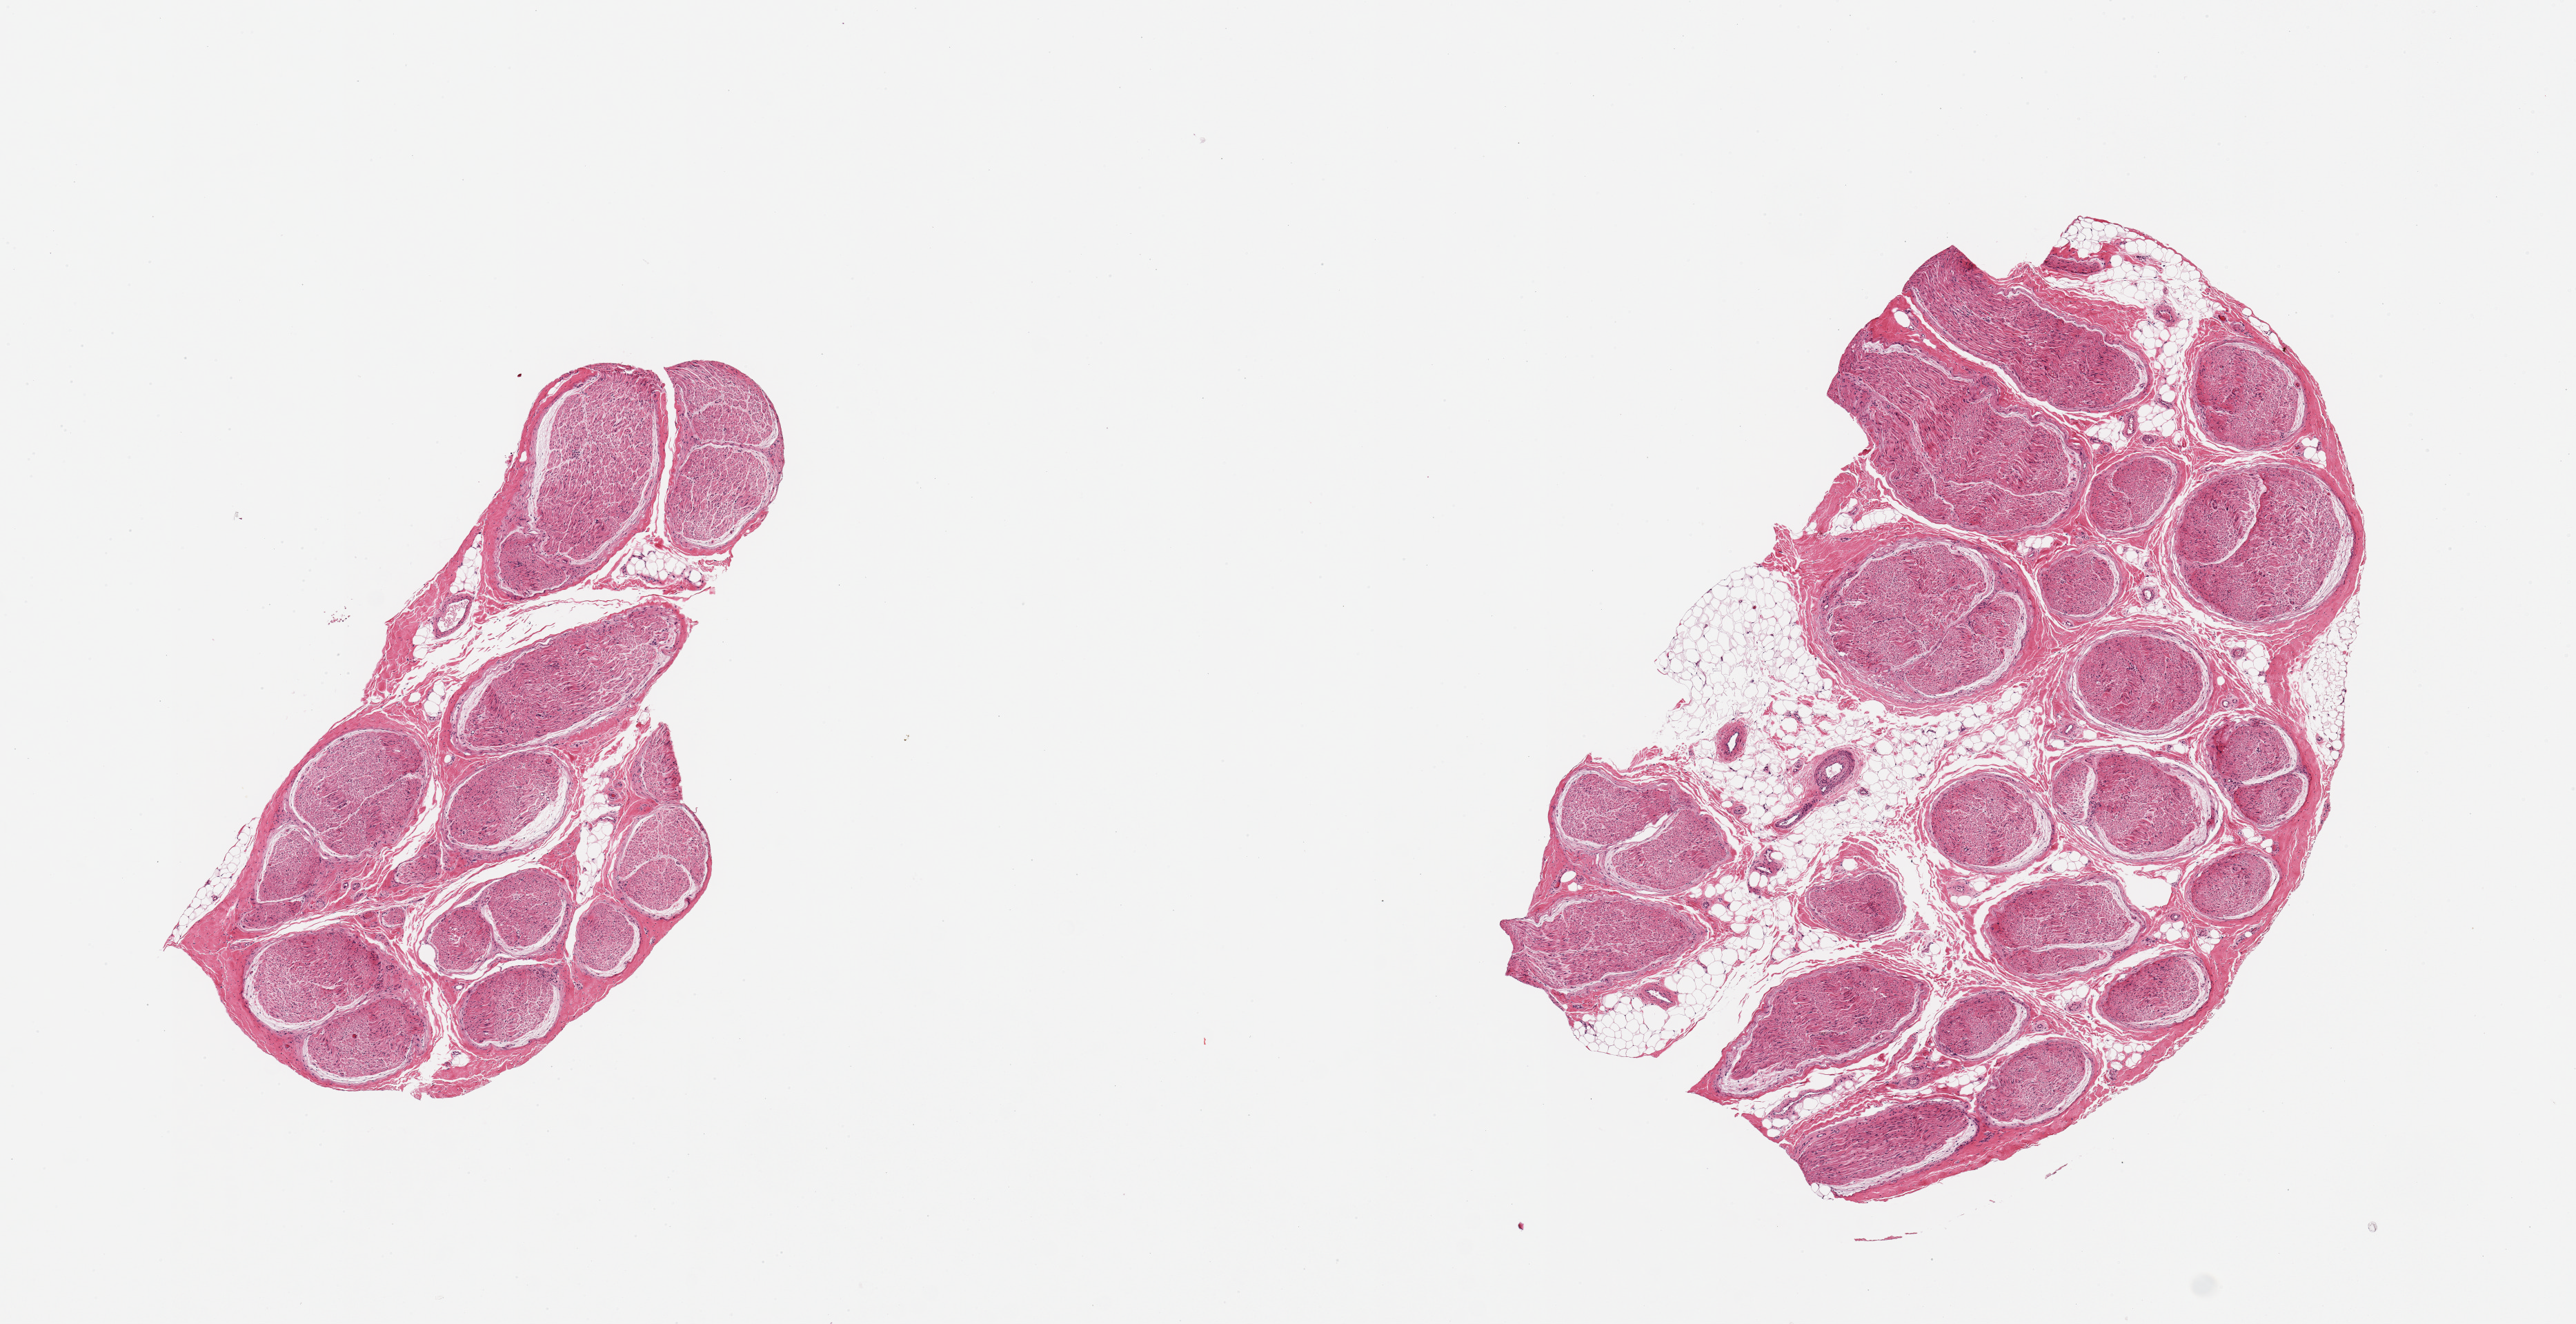
Hematoxylin and eosin (H&E) whole-slide image, low-resolution overview of the scanned area, about 14.8 x 7.6 mm. PAXgene-fixed paraffin-embedded (PFPE) section. Section of tibial nerve (target tissue). Tissue donor sample. Male donor.
Reviewer comment on this tissue sample: 2 pieces; 5 to 10% internal fat.